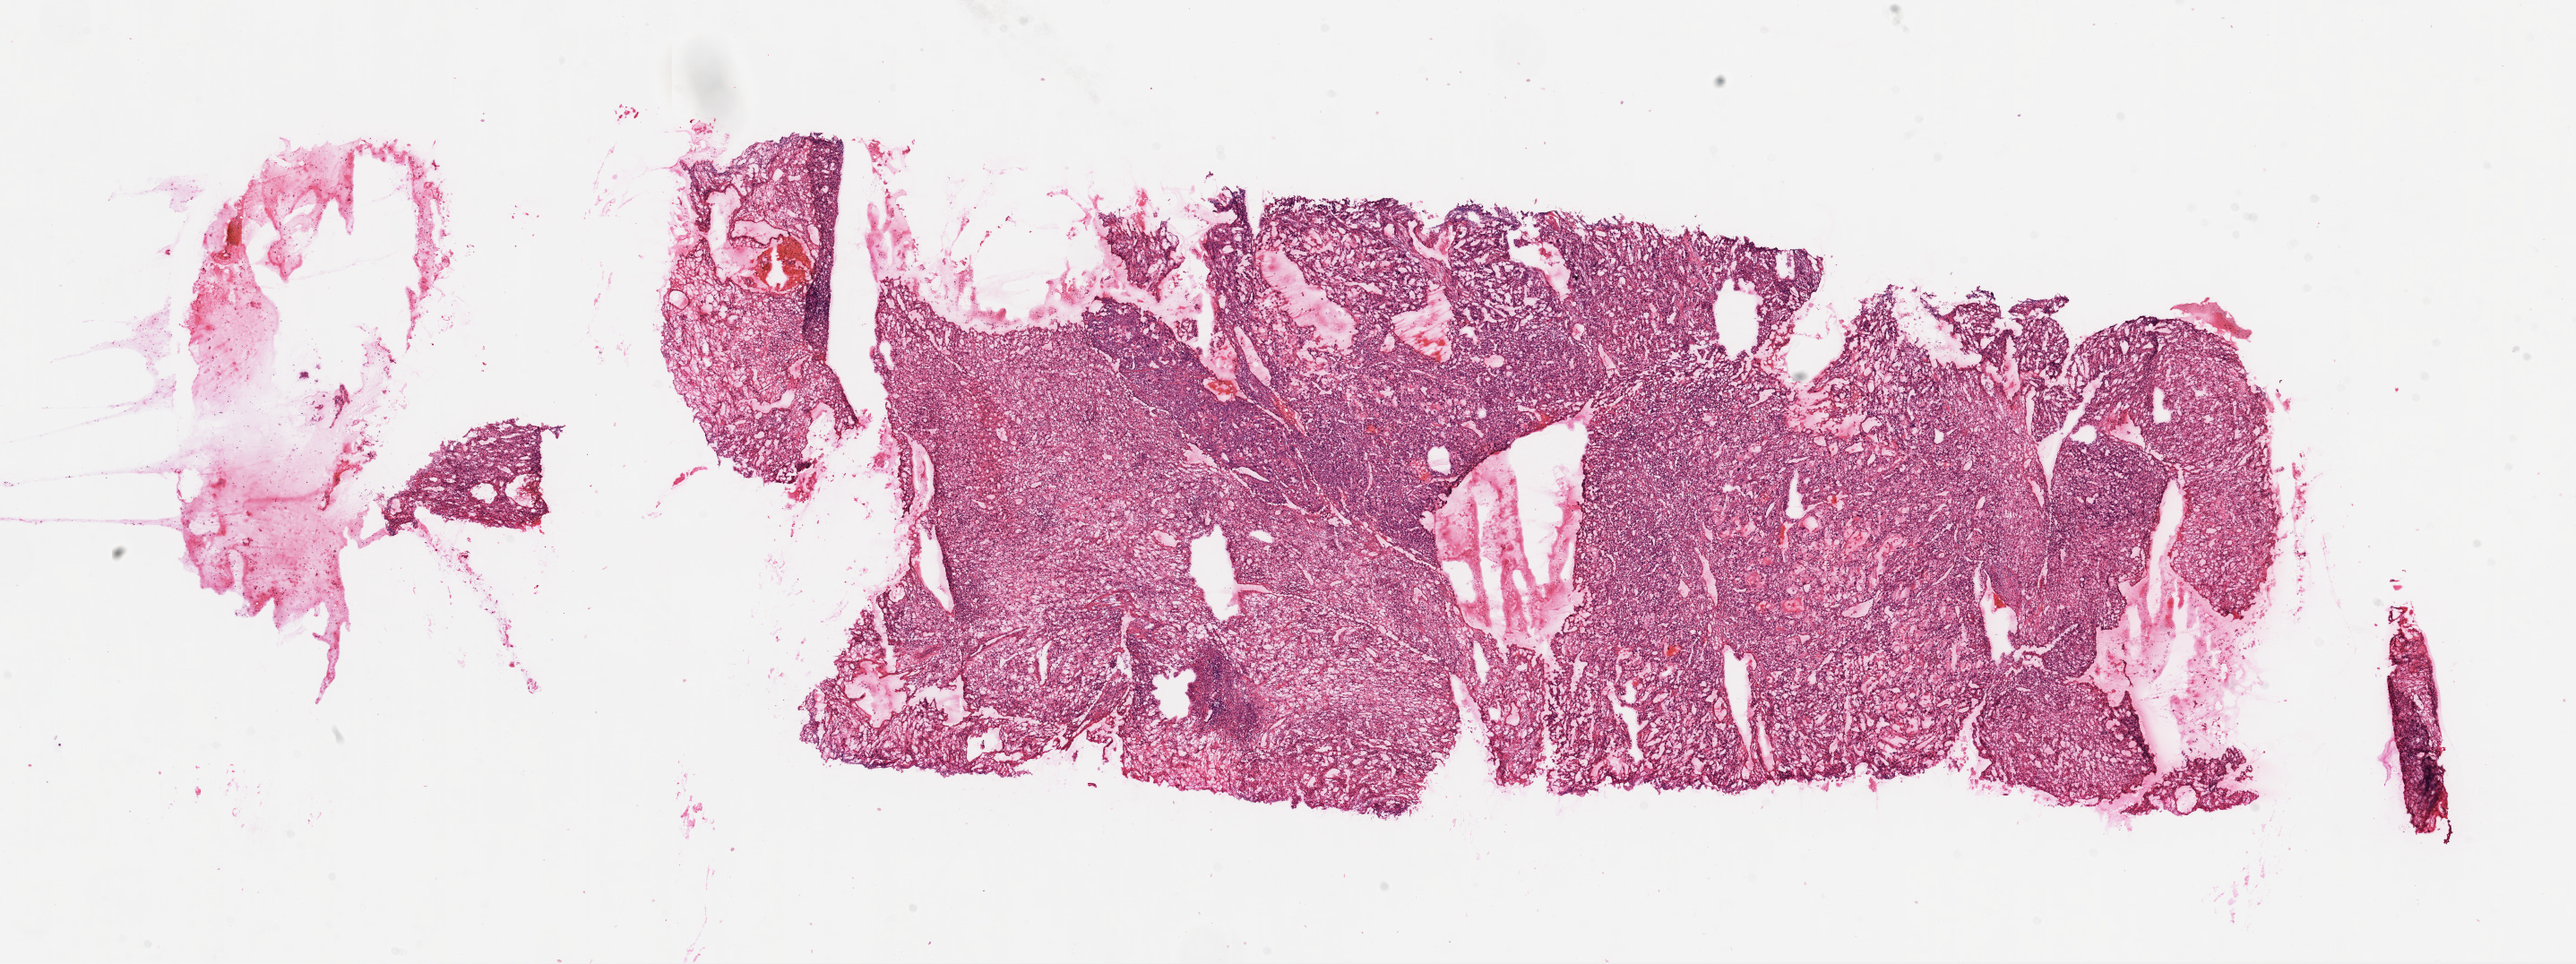
Whole-slide histology image, H&E — whole scanned area (about 23.1 x 8.6 mm) shown as a low-resolution overview, frozen section from the top of the tissue portion, kidney, primary tumour sample. Male, age 51 years at initial diagnosis. Histologic grade: G4 (undifferentiated). Pathologist review of this section (percent, as recorded): tumour cells 90%, tumour nuclei 90%, normal cells 0%, stromal cells 10%, necrosis 0%.
* AJCC pathologic stage: I
* diagnosis: Clear cell adenocarcinoma, NOS
* lymph nodes positive (case pathology): 0 of 1 examined
* laterality: right